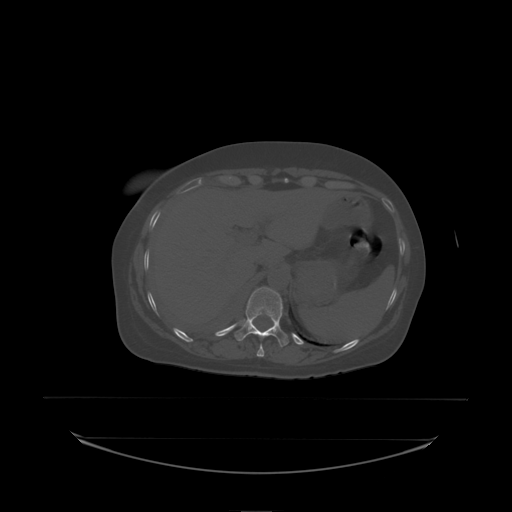
CT including the spine, one axial slice; slice 105 of 242 in the series (ordered by position); bone window (W 1800 / L 400 HU); 2.5 mm slice thickness; 512 × 512 image matrix, field of view 500 × 500 mm. Female patient, age 53 years. From the clinical record (not read from this slice): primary cancer: lung; vertebrae with lytic lesions (as recorded): T7, L1.
Annotated regions visible in this slice (semi-automatic segmentation, software-assisted and operator-edited):
- T11 vertebra: bounding box (x1, y1, x2, y2) in pixels: (236, 287, 285, 338)